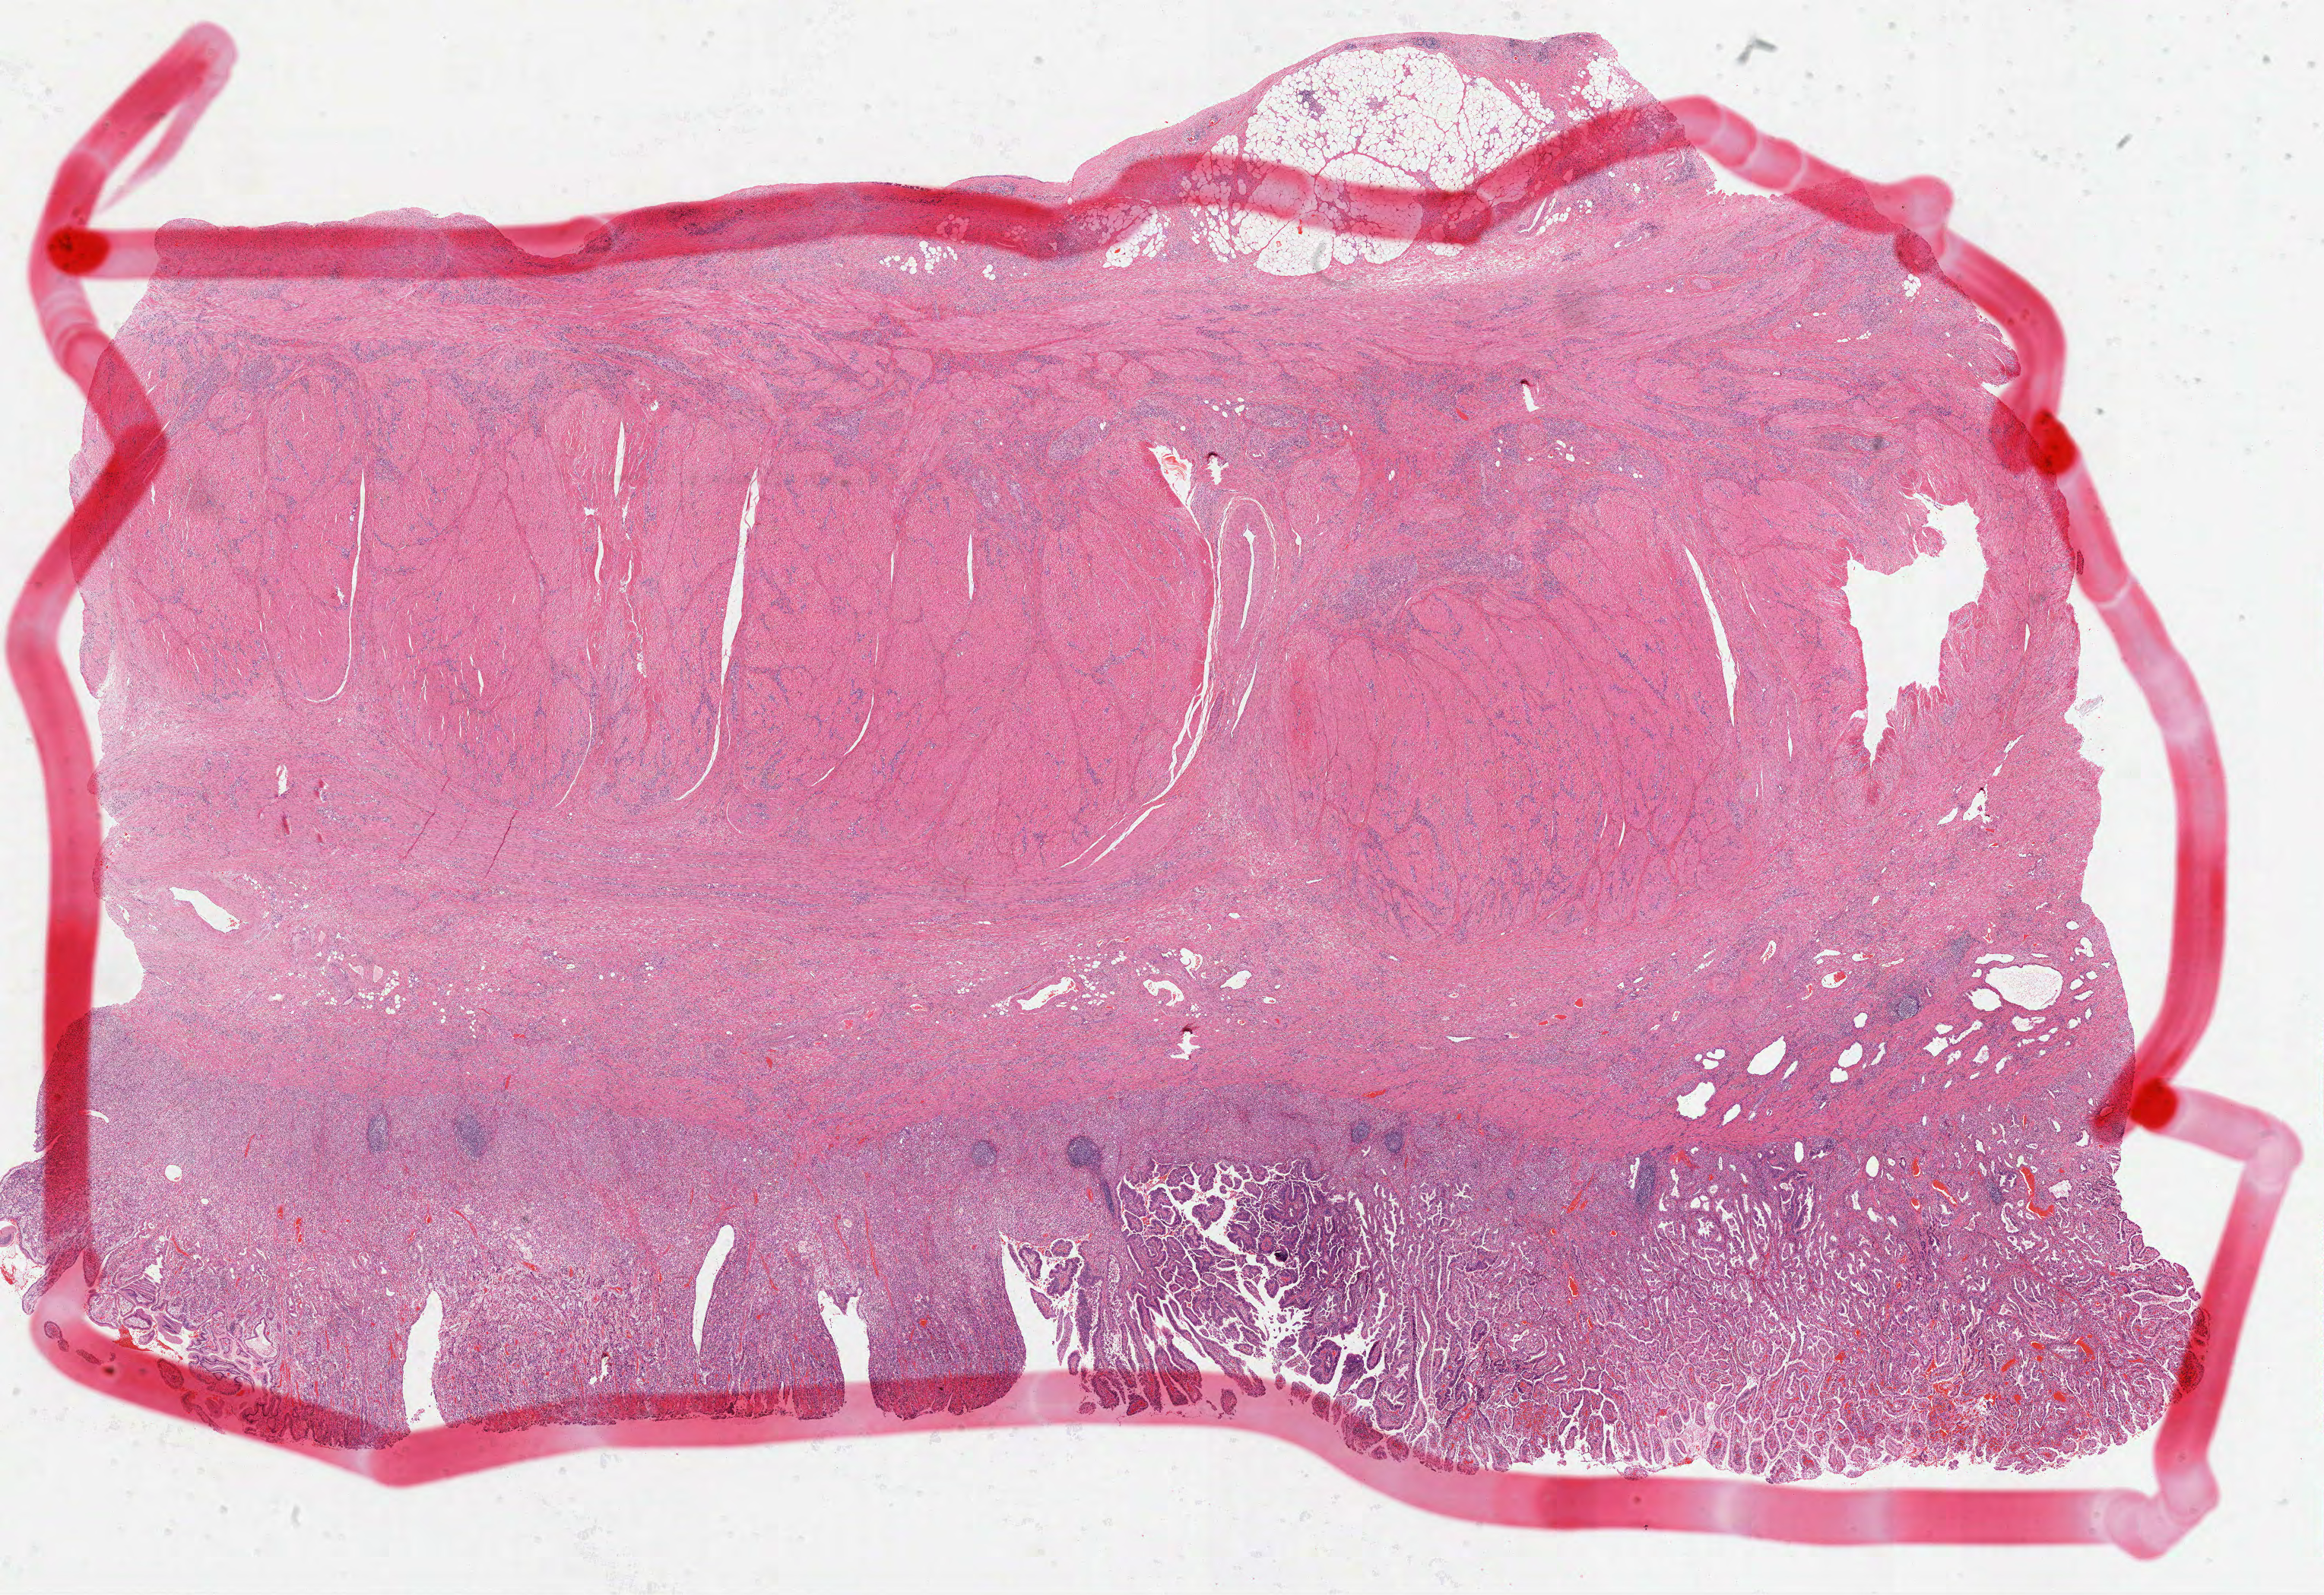
Digitized H&E-stained tissue section (whole slide), a low-resolution overview of the entire scanned area, about 24.7 x 16.9 mm (from a 40x scan), FFPE section, stomach, primary tumour sample. Male, age 58 years at initial diagnosis. Histologic grade: GX (grade cannot be assessed).
Diagnosis: Carcinoma, diffuse type. AJCC pathologic stage: IIIC (7th edition).